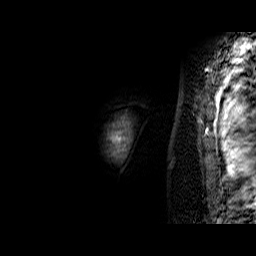
Breast MRI (dynamic contrast-enhanced), one sagittal slice. Dynamic contrast-enhanced series, time point 2 of 6 at this slice position (early post-contrast). 1.5 T. TE 6.4 ms, TR 32.9 ms. 4 mm slice thickness. 256 × 256 image matrix, field of view 200 × 200 mm. Female patient. From the clinical record (not read from this slice): setting: breast cancer imaged before/during neoadjuvant chemotherapy; receptor status: triple-negative.
Structures marked on this image (semi-automatic segmentation, software-assisted and operator-edited):
- analysis volume of interest (the breast-tissue region the enhancement analysis was run in; not a lesion): bounding box [x1, y1, x2, y2] px = [108, 121, 132, 160]
- tumour enhancement mask (voxels above the 100 % enhancement threshold inside the analysis volume of interest): [110, 121, 132, 158]